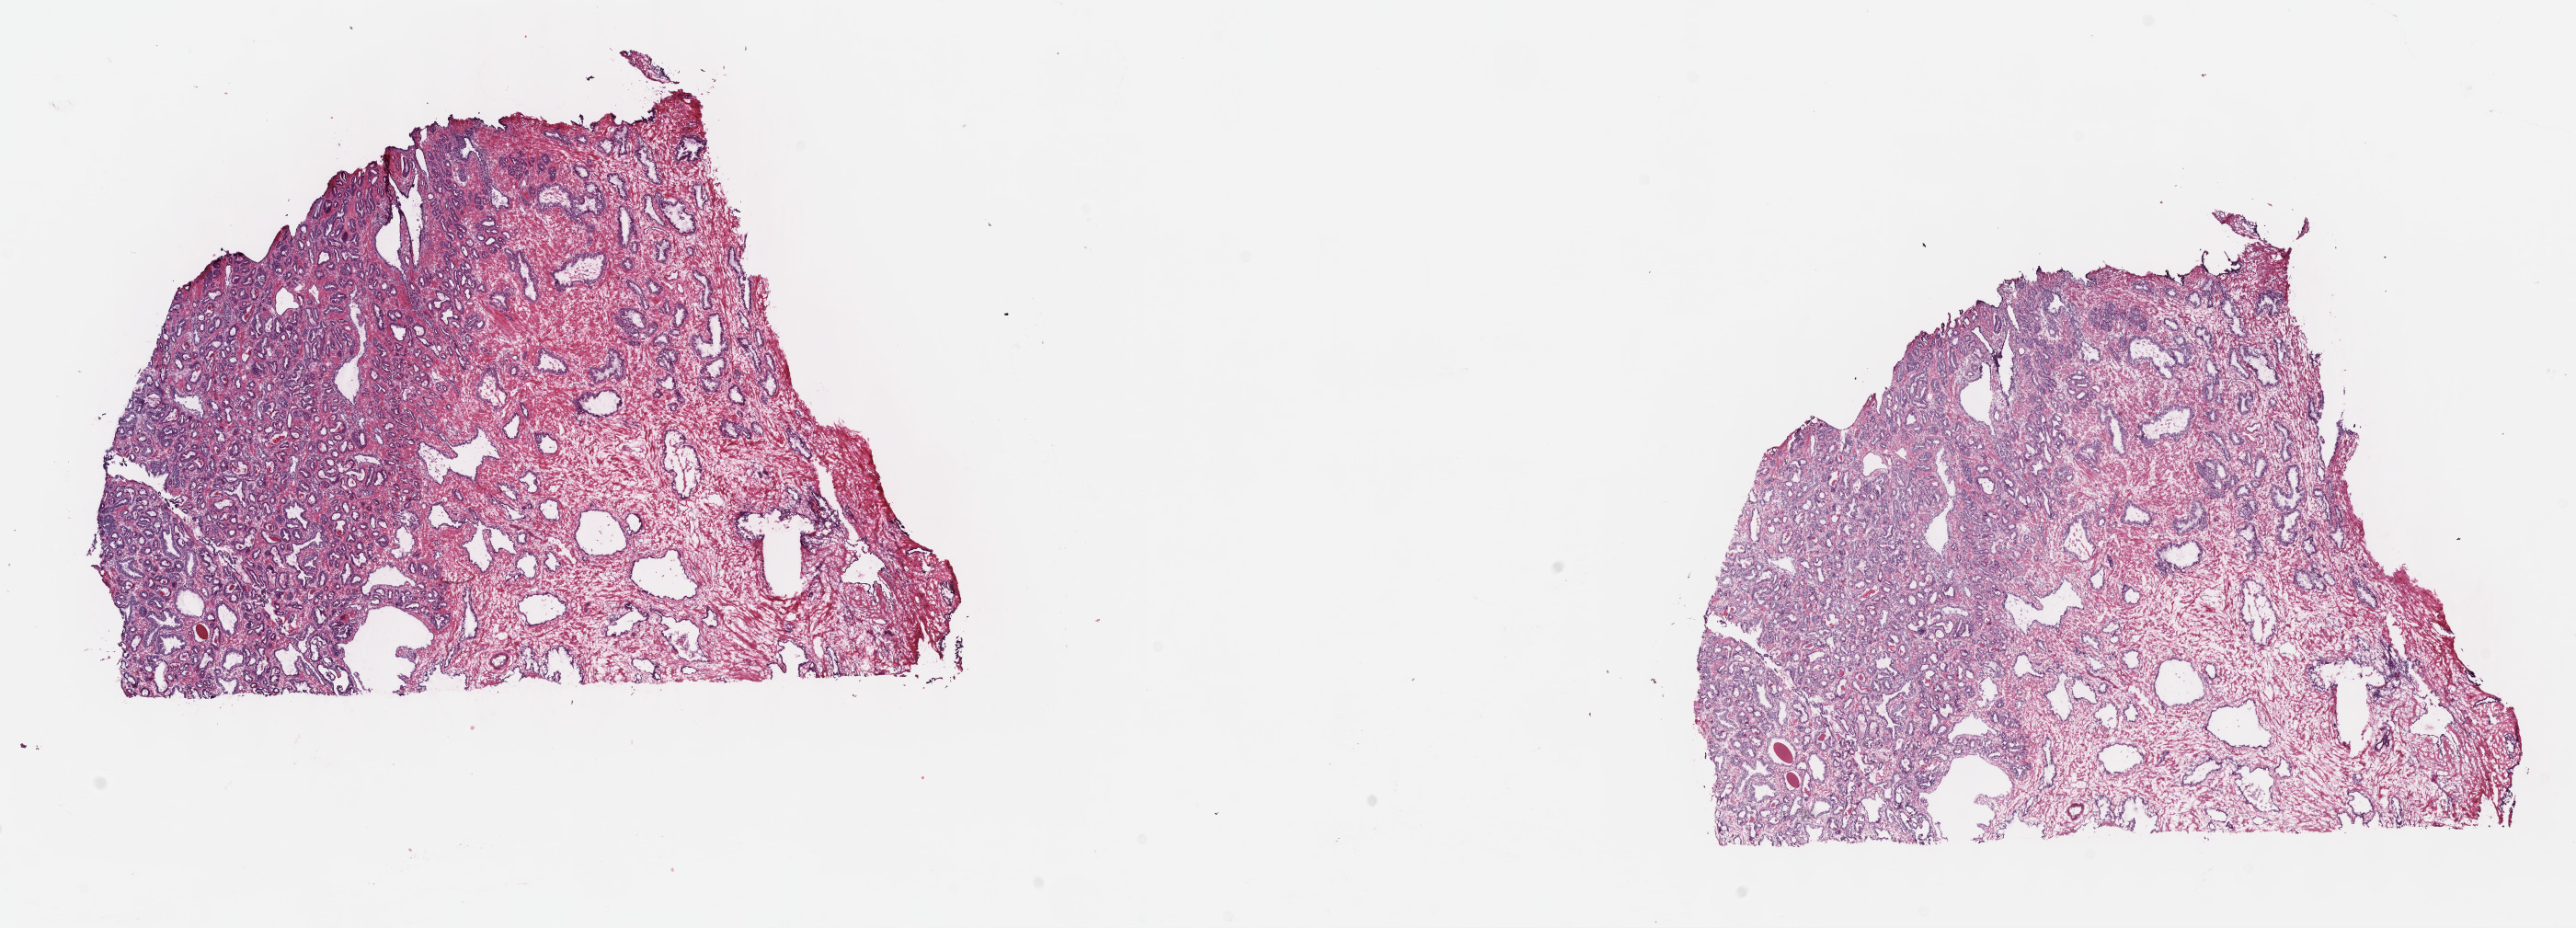
Whole-slide histology image, H&E-stained — whole scanned area (about 22.7 x 8.2 mm) shown as a low-resolution overview, frozen section, prostate, primary tumour sample. Male patient; age at initial diagnosis 56 years. Gleason score: 7 (3+4). Composition of this section per pathologist review: tumour cells 45%, tumour nuclei 60%, normal cells 15%, stromal cells 40%, necrosis 0%. Inflammatory infiltration, as recorded: lymphocyte infiltration 0%, monocyte infiltration 0%, neutrophil infiltration 0%.
Histologic diagnosis: Adenocarcinoma, NOS (prostate gland).